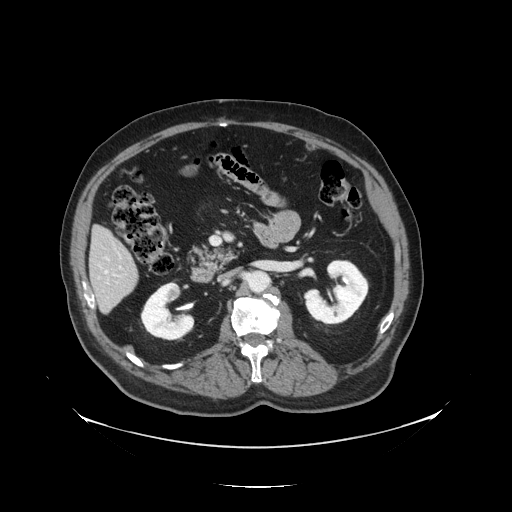
Contrast-enhanced abdominal CT, one axial slice; position 54 of 138 along the scan axis; reconstruction kernel STANDARD; intravenous contrast given; soft-tissue window (W 400 / L 40 HU); 2.5 mm slice thickness; 512 × 512 image matrix, field of view 497 × 497 mm. Male patient, age 77 years. From the clinical record (not read from this slice): diagnosis: colorectal cancer liver metastases, imaged before liver resection; multiple liver metastases: no; largest metastasis: 1.5 cm; disease in both lobes: no.
Annotated regions visible in this slice (outlined manually by an expert reader):
- liver: bounding box <91,229,139,311> (left, top, right, bottom; pixels)
- planned liver remnant (the part of the liver to remain after resection): <92,229,137,282>